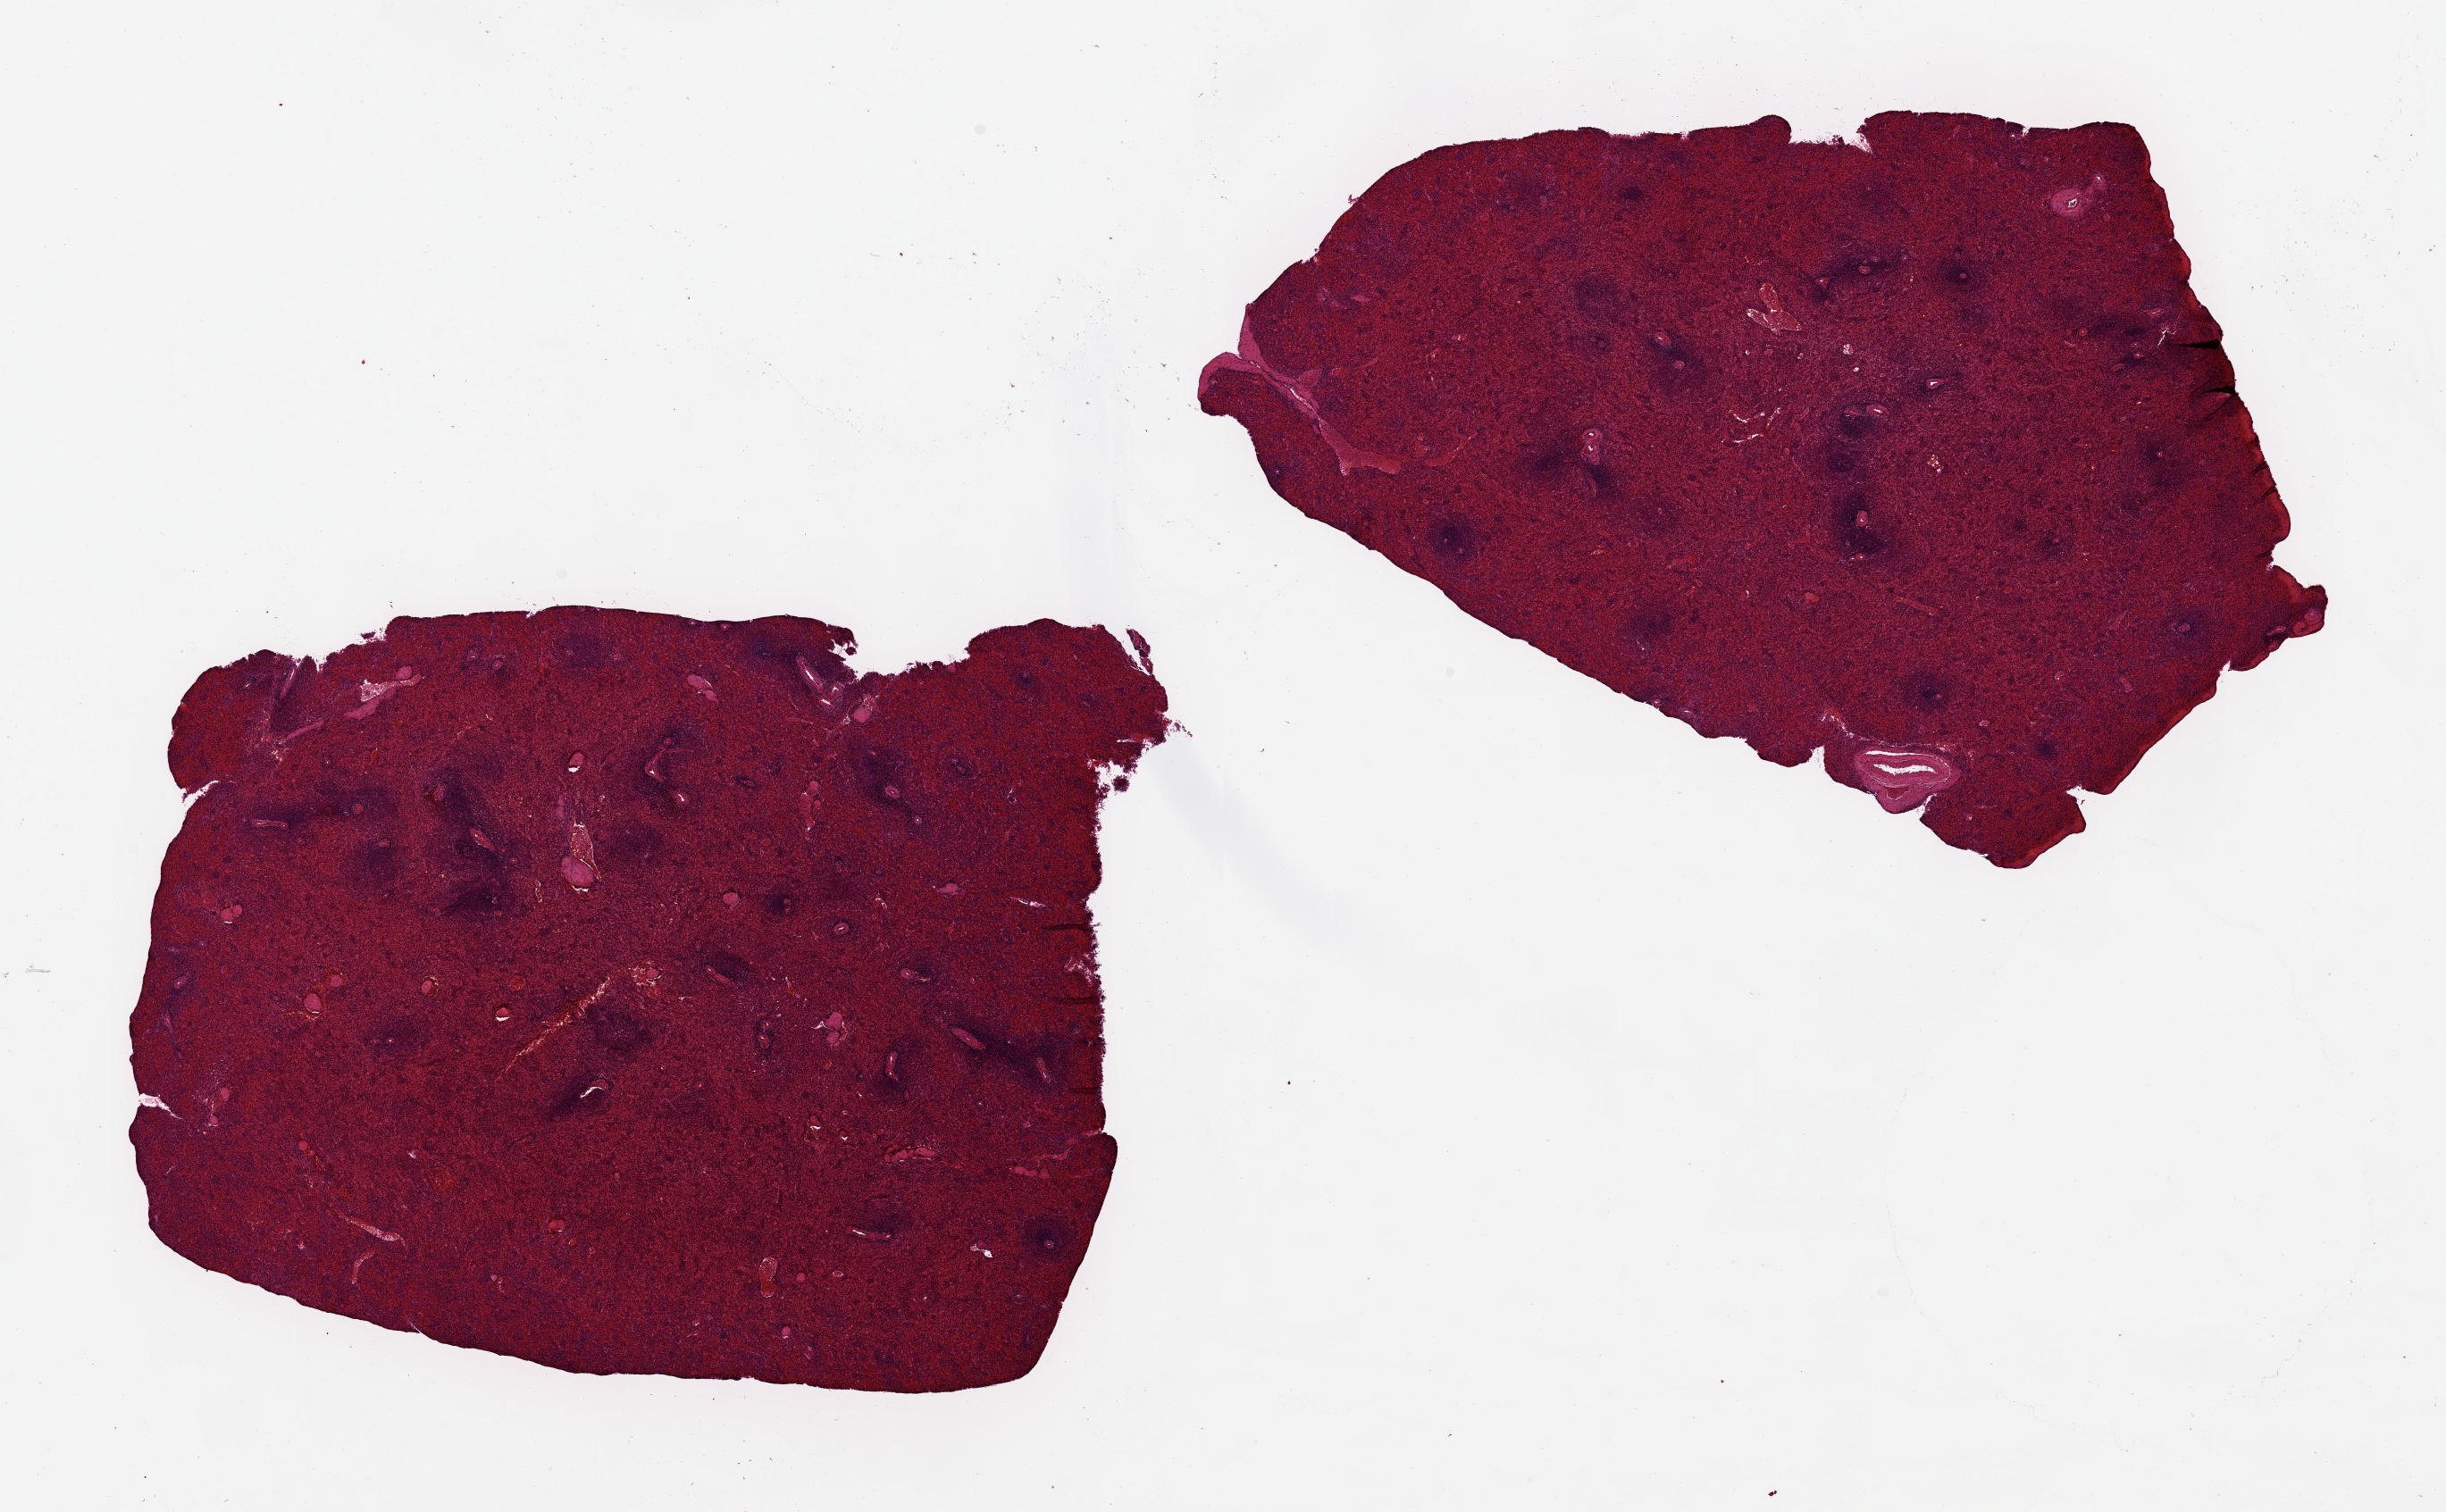
Haematoxylin and eosin whole-slide image — a low-resolution overview of the entire scanned area, about 21.7 x 13.4 mm; PAXgene-fixed paraffin-embedded (PFPE) section; sampled site (target tissue): spleen; donor tissue sample. Female donor.
• reviewer comment on this tissue sample: 2 pieces, 6x8mm; moderately congested